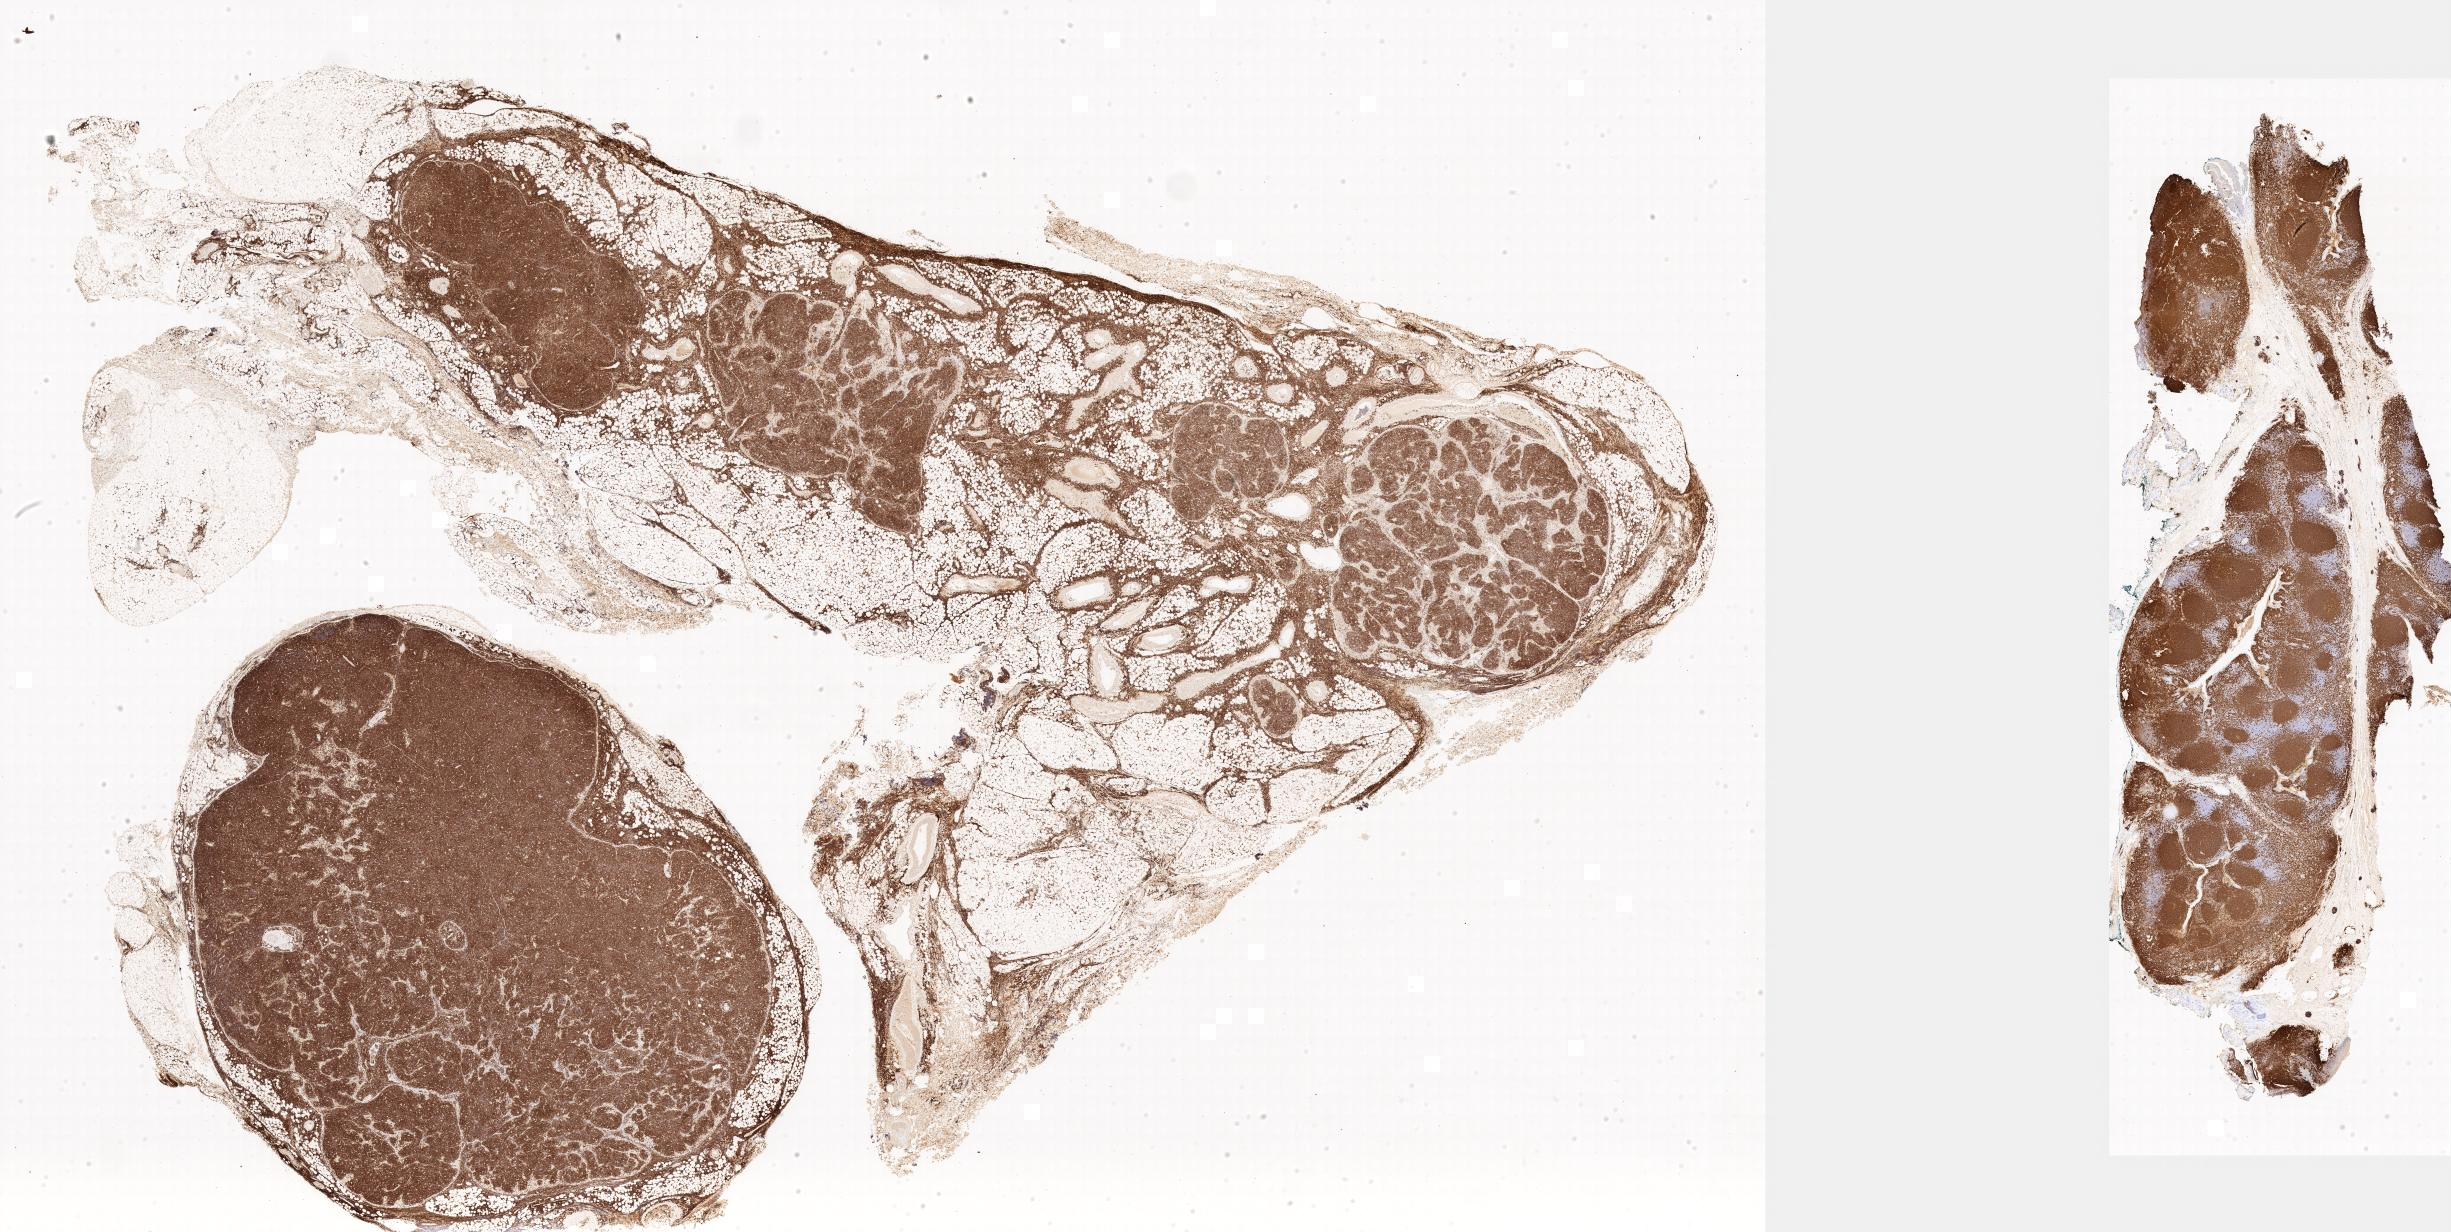
Immunohistochemistry (IHC) whole-slide image stained for CD20 — a low-resolution overview of the entire scanned area, specimen: tumor tissue, anatomic site: spleen. Patient: female, 15 years old.
* diagnosis: Burkitt lymphoma, NOS